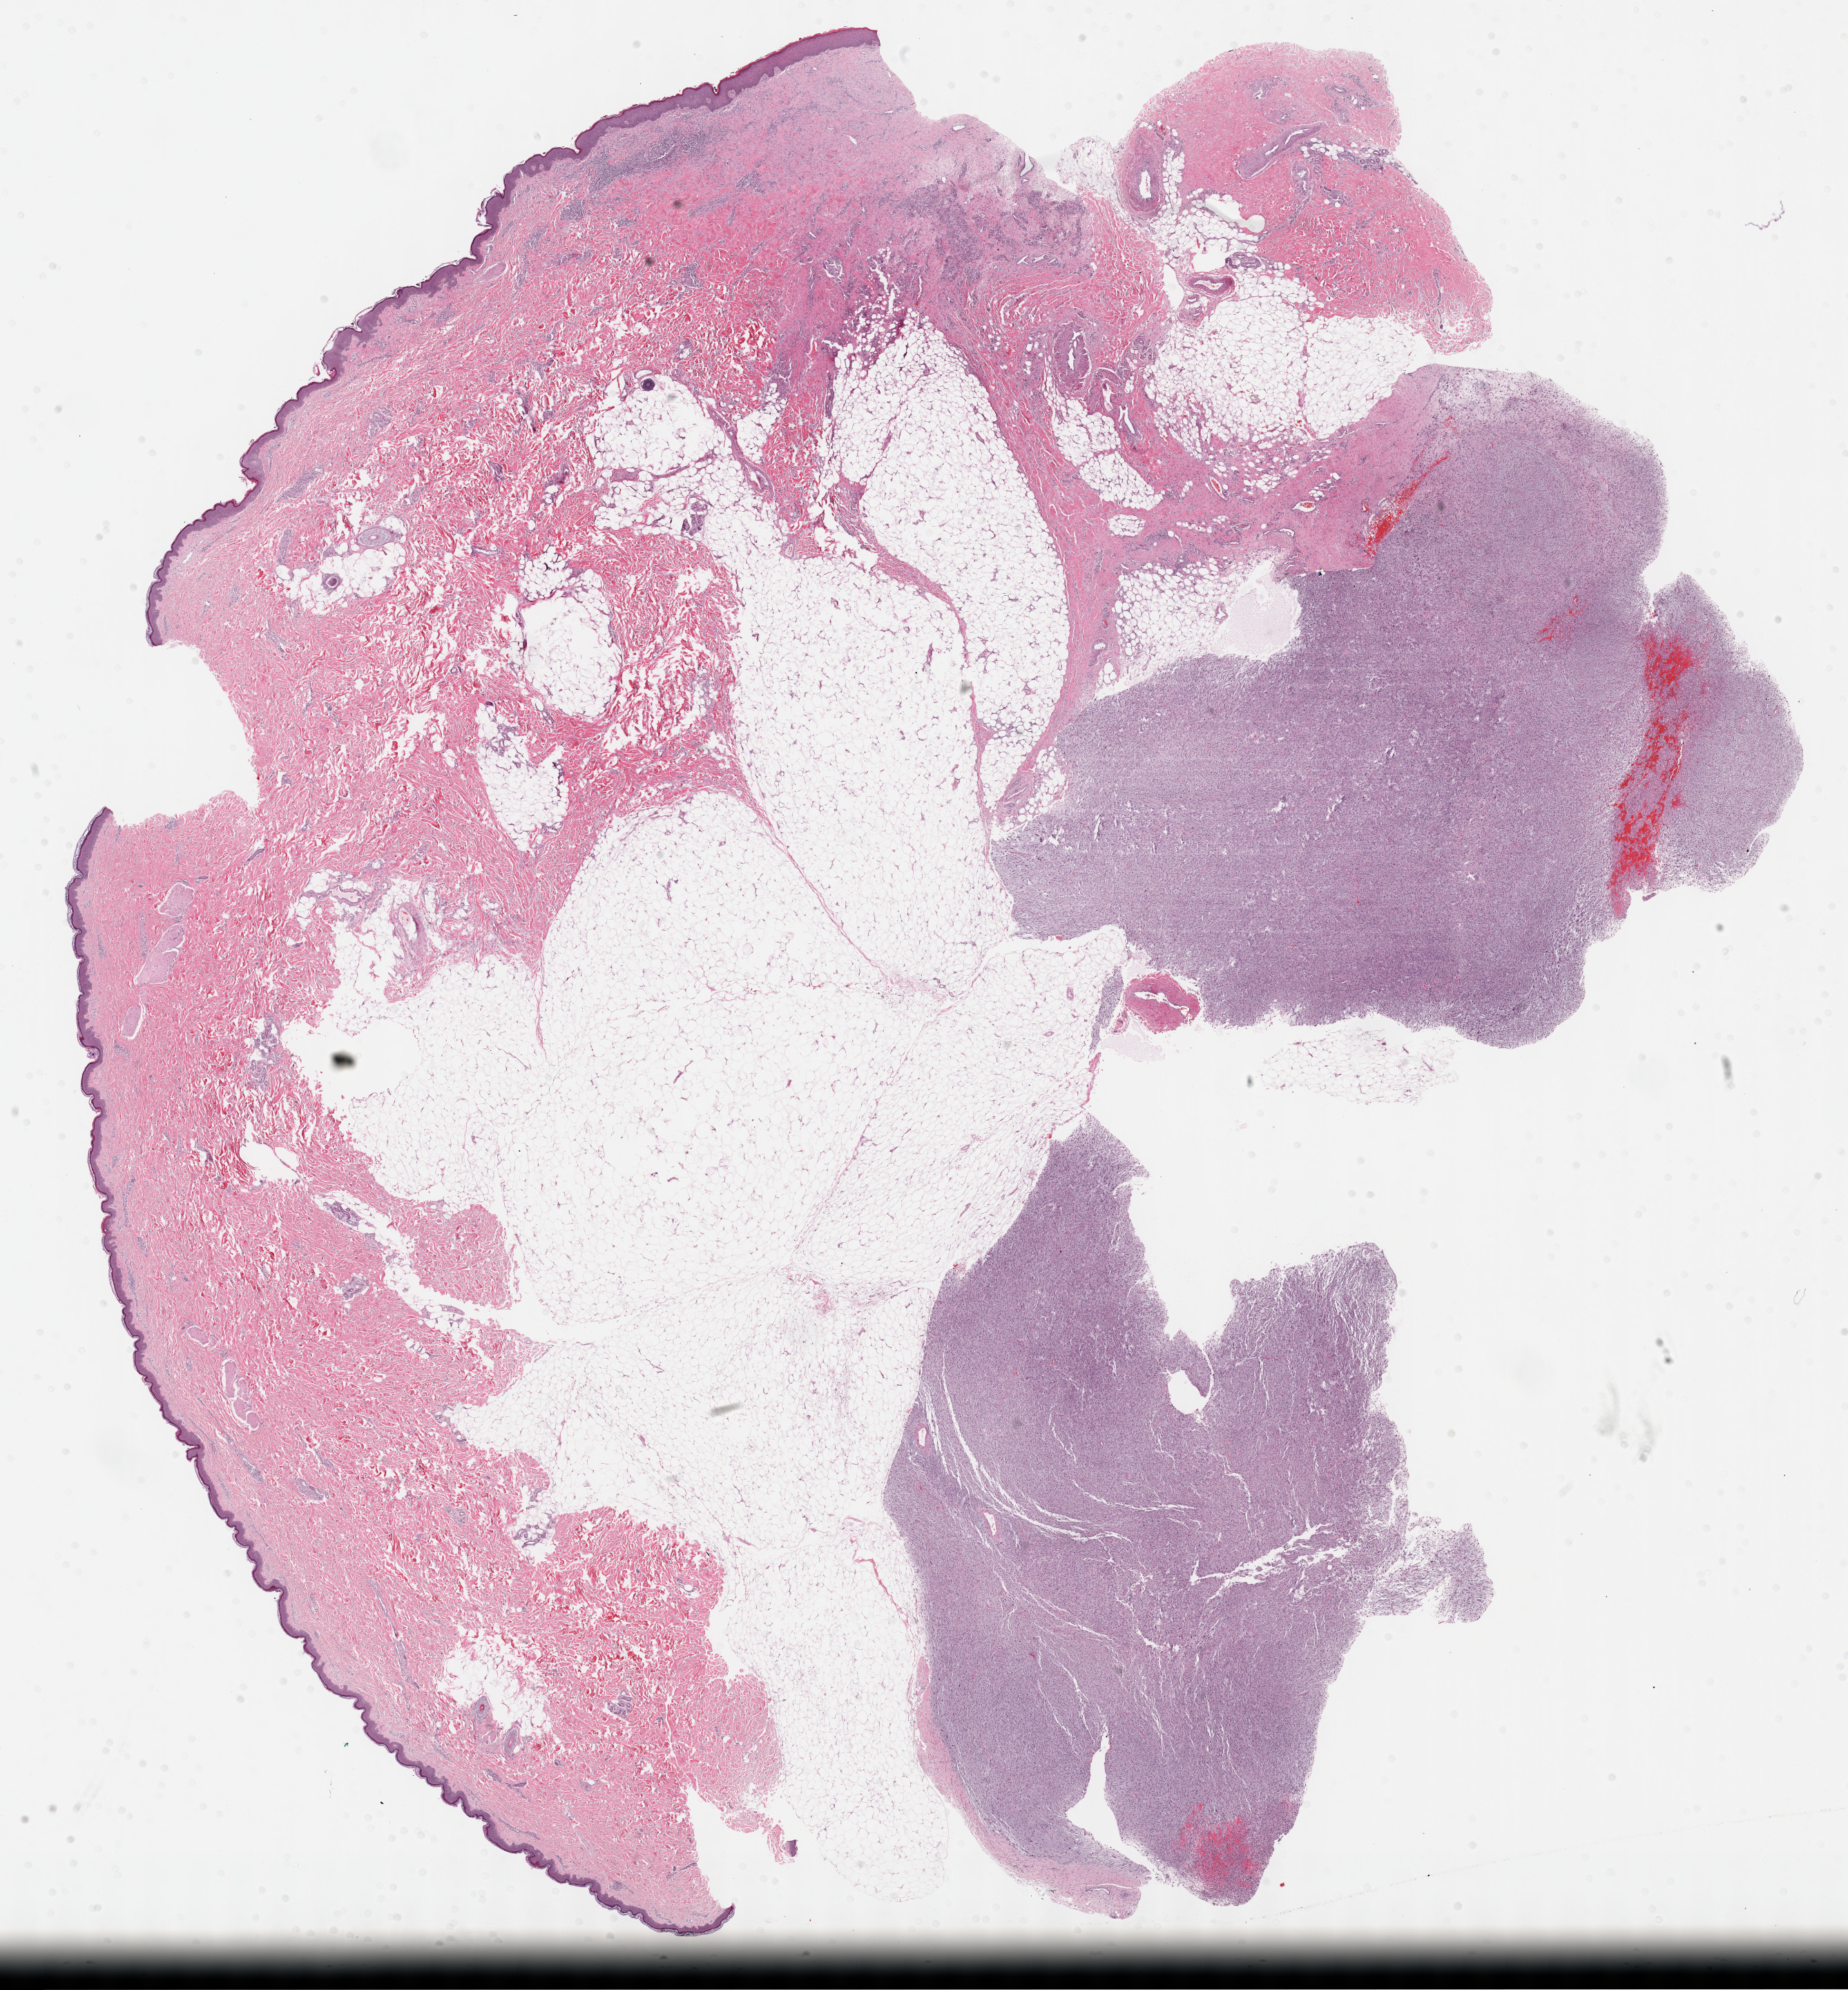
Digitized H&E tissue section (whole slide), low-resolution overview of the scanned area, about 21.6 x 23.3 mm, formalin-fixed paraffin-embedded (FFPE) diagnostic section, primary tumour sample from the connective, subcutaneous and other soft tissues. Female patient; age at initial diagnosis 31 years.
Histologic diagnosis: Fibromyxosarcoma (connective, subcutaneous and other soft tissues of lower limb and hip).